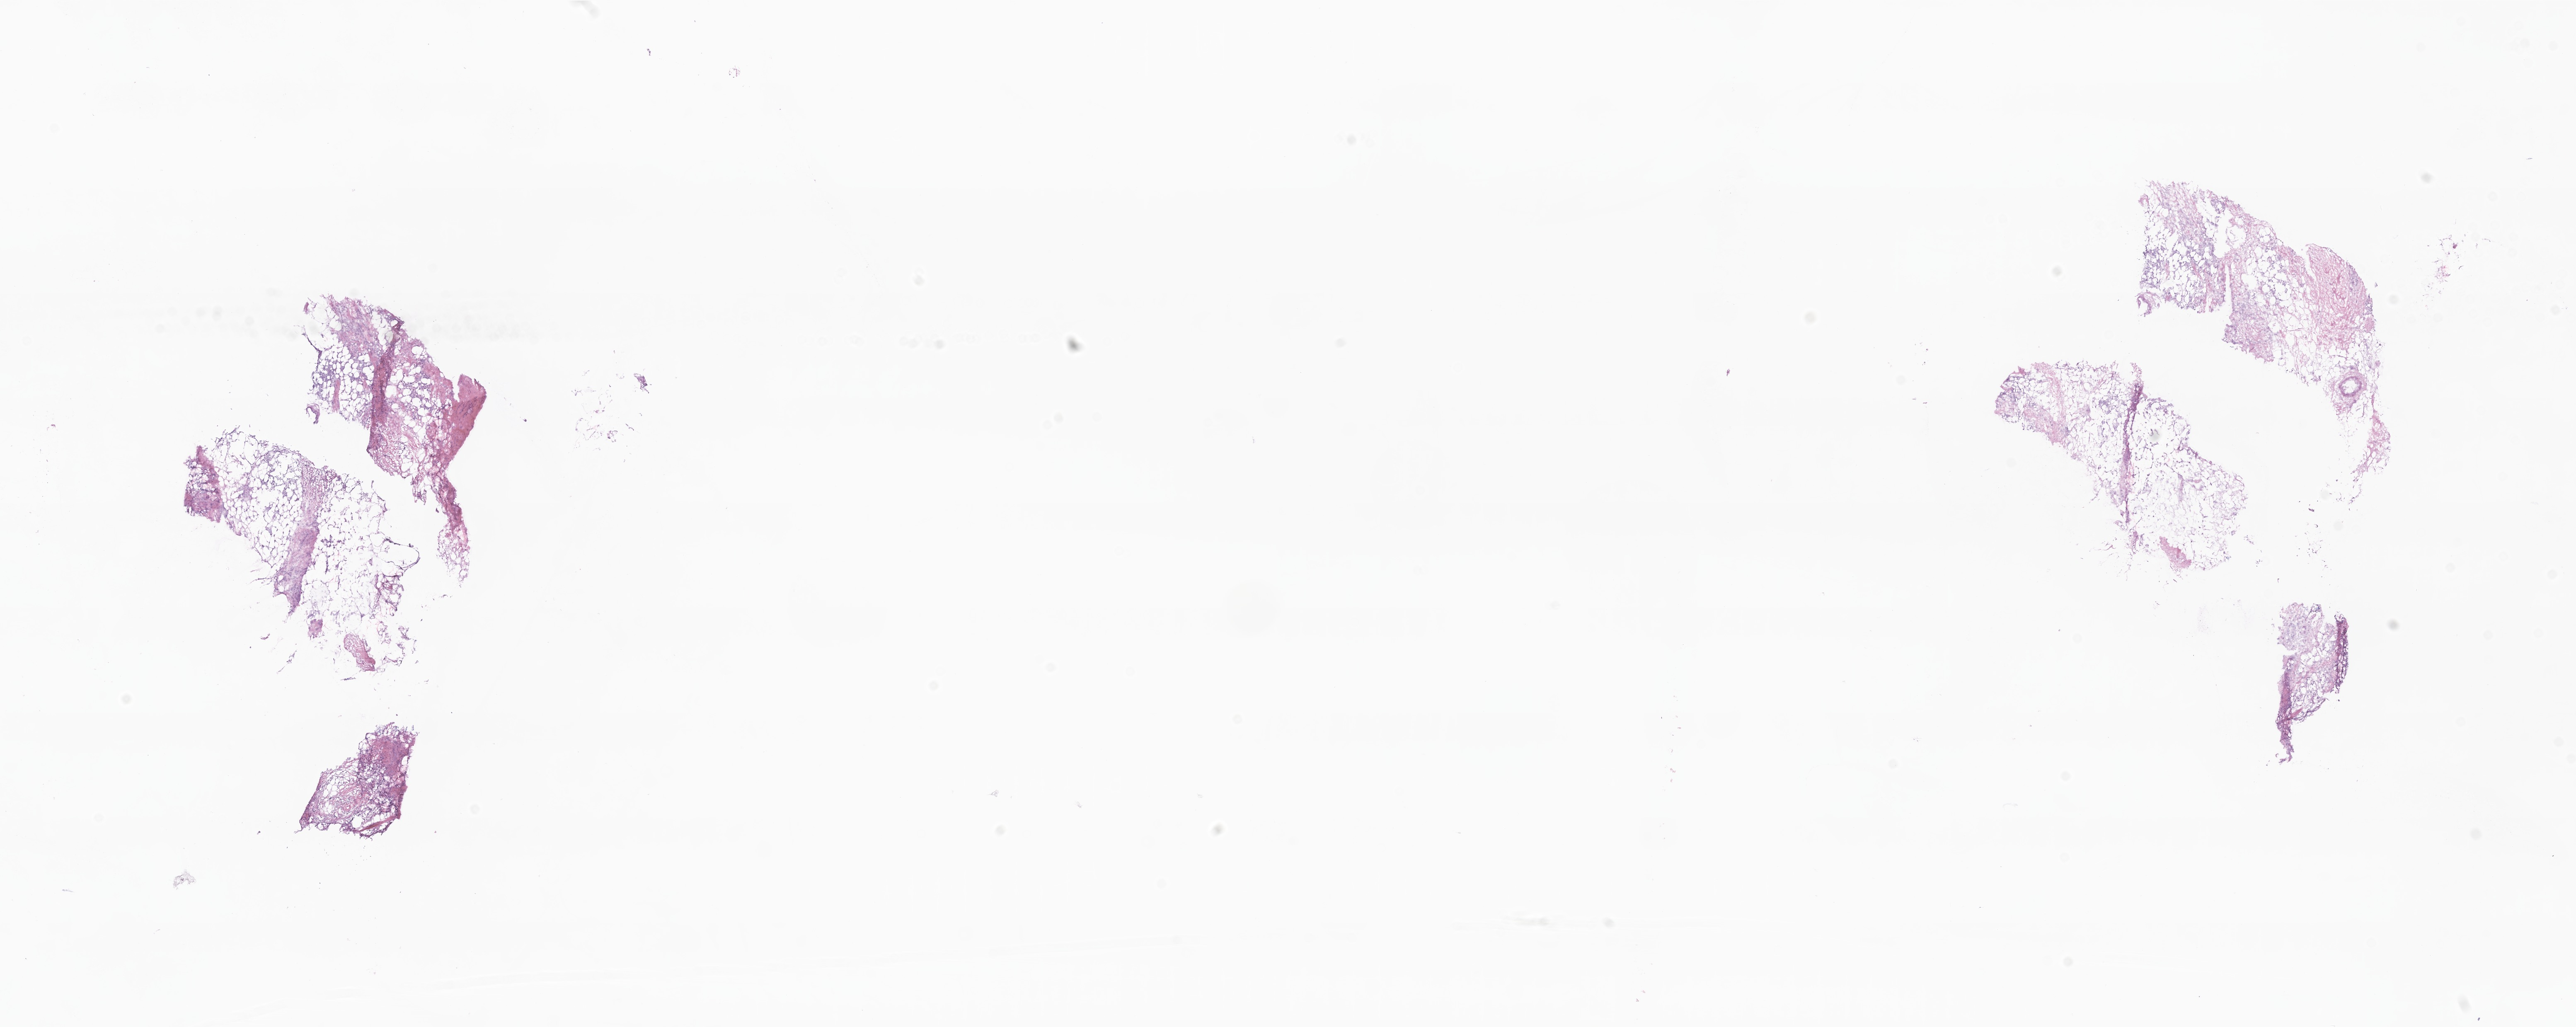
Whole-slide image, H&E stain — low-resolution overview of the scanned area, about 26.2 x 10.4 mm, frozen section (tissue freezing medium), specimen: primary tumor, site: breast. Female, age 62 years at initial diagnosis. Pathologist review of this section (percent, as recorded): tumor cells 95%, tumor nuclei 80%, stromal cells 0%, necrosis 0%, normal cells 5%. Infiltration values recorded for this section: lymphocyte infiltration 0%, monocyte infiltration 0%, neutrophil infiltration 0%.
Diagnosis: Lobular carcinoma, NOS. Section: bottom of the tissue portion.